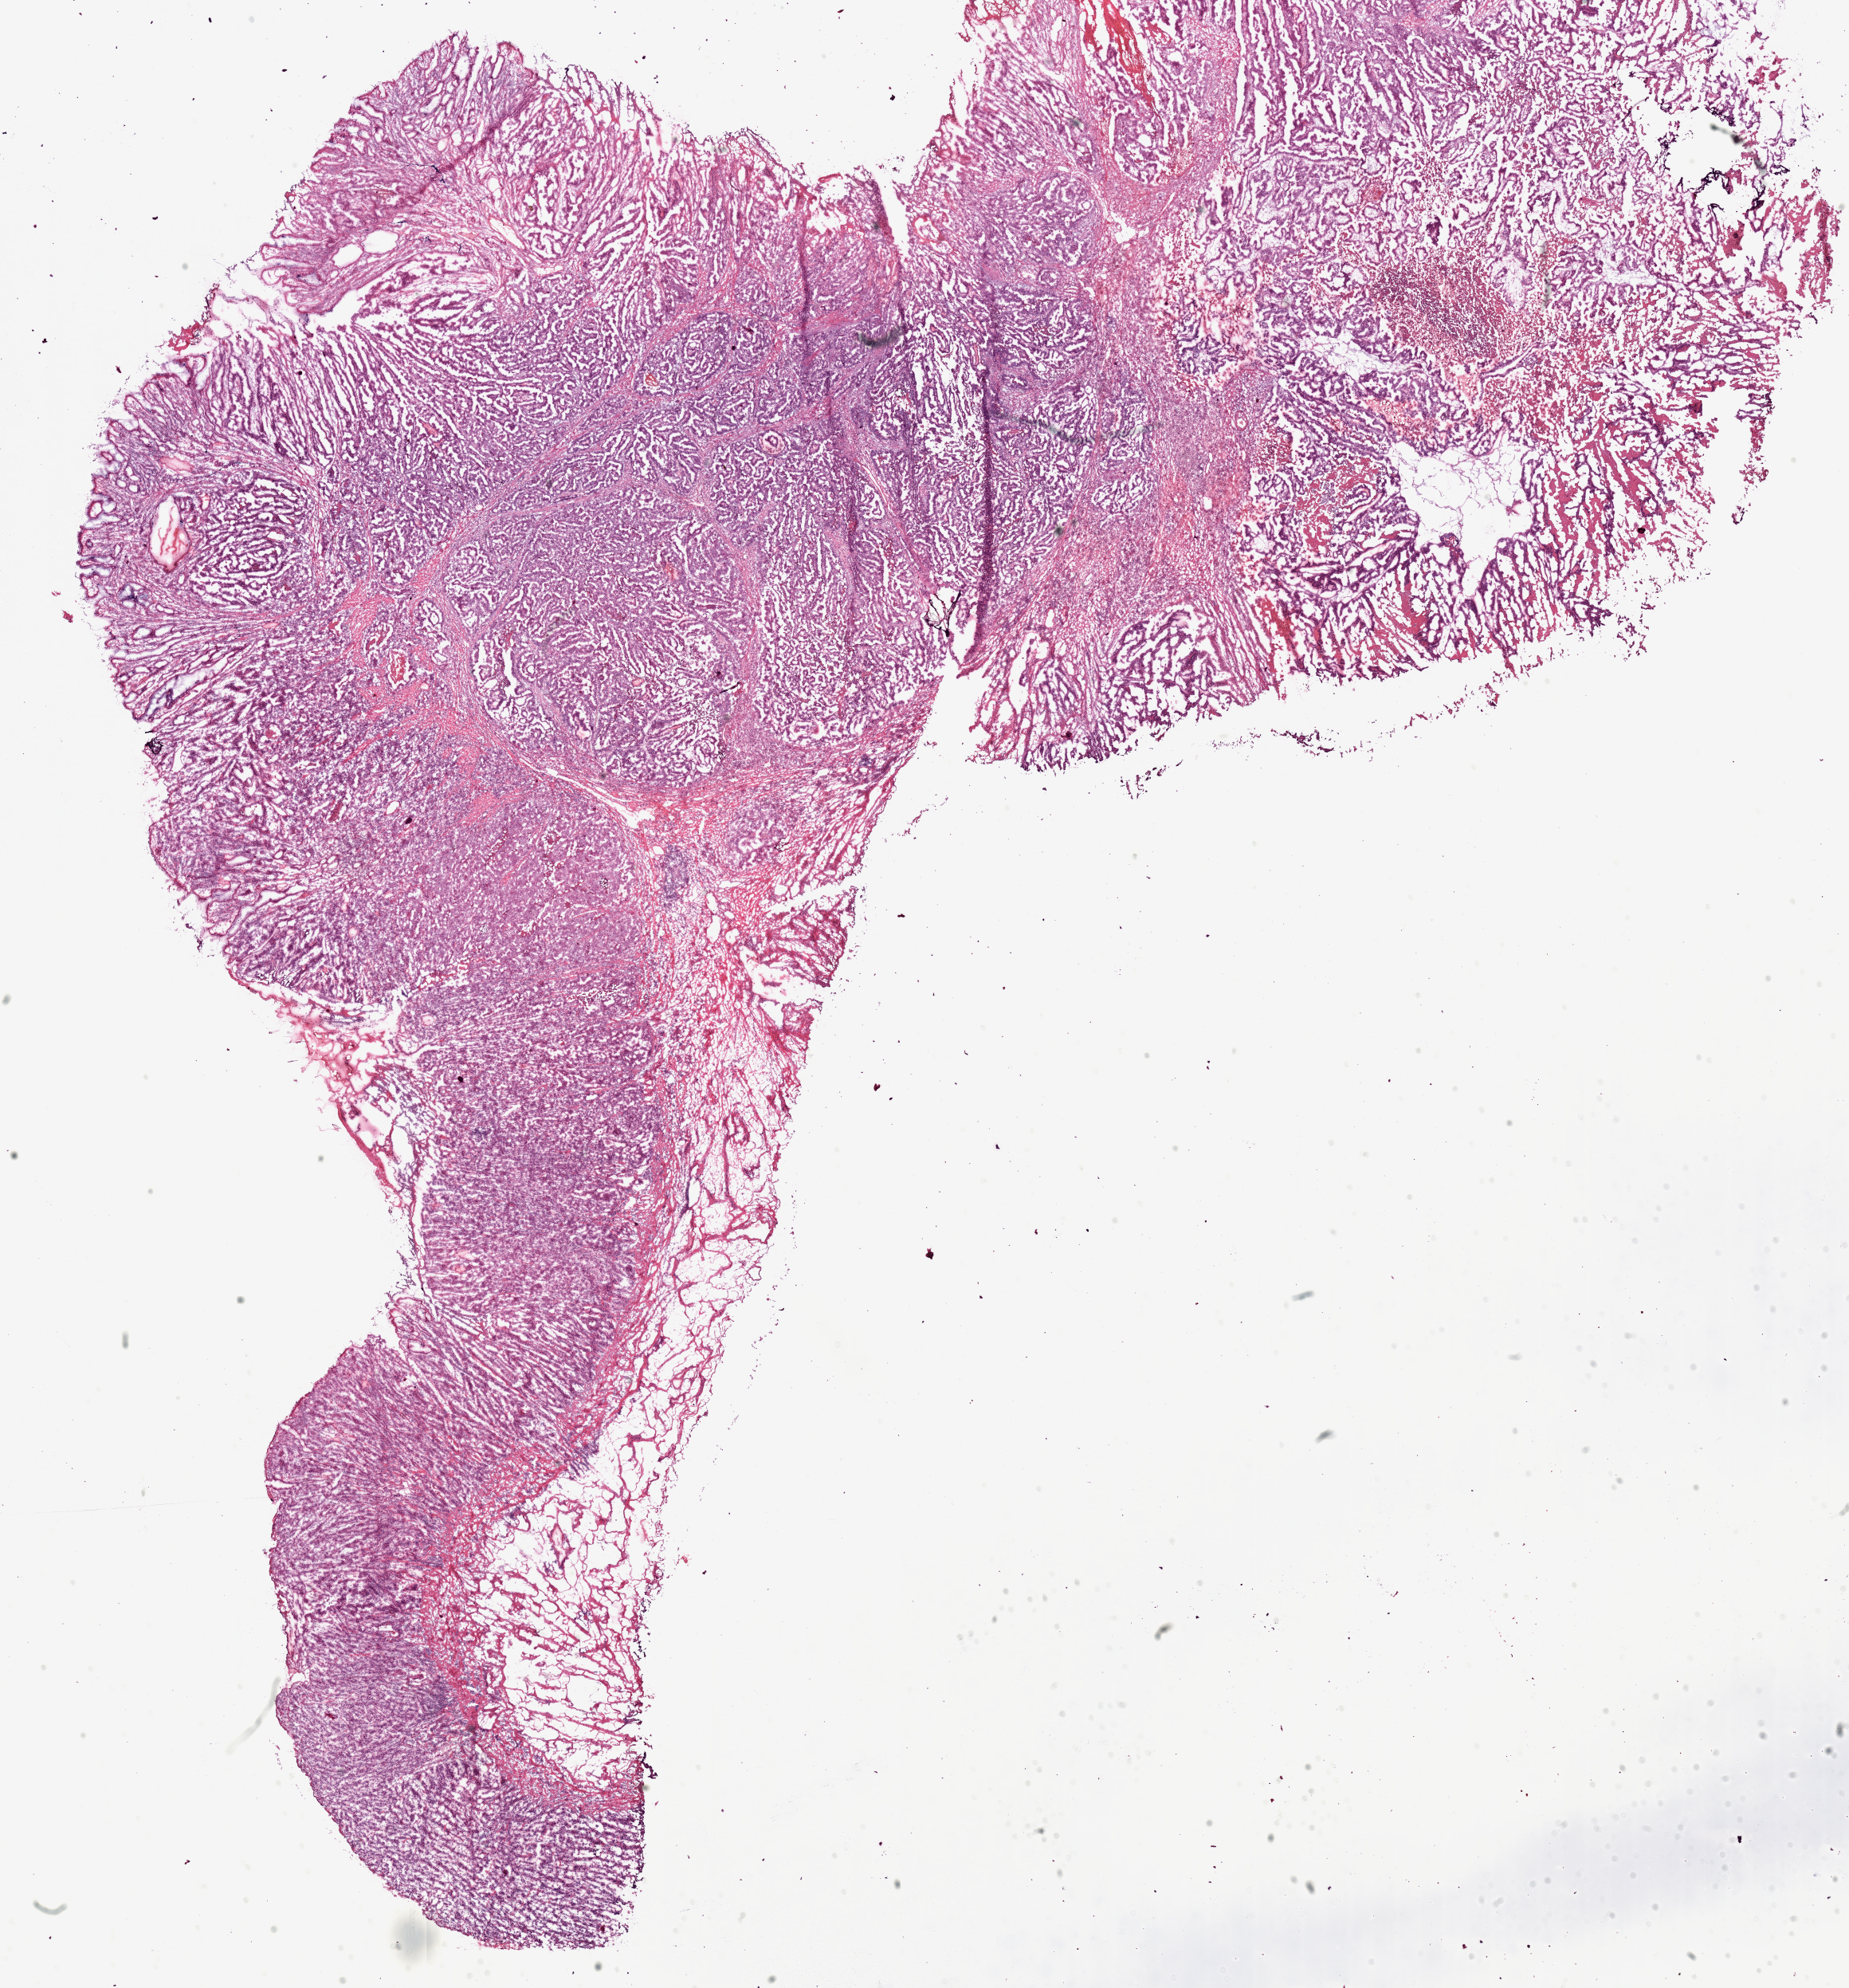
Digitized H&E tissue section (whole slide), a low-resolution overview of the entire scanned area, about 18.4 x 19.8 mm. Frozen section from the top of the tissue portion. Primary tumour sample from the stomach. Female patient; age at initial diagnosis 51 years. Histologic grade: G1 (well differentiated). Pathologist review of this section (percent, as recorded): tumour cells 80%, tumour nuclei 80%, normal cells 0%, stromal cells 10%, necrosis 10%.
AJCC pathologic stage: II (6th edition). Pathologic diagnosis: Papillary adenocarcinoma, NOS (gastric antrum).